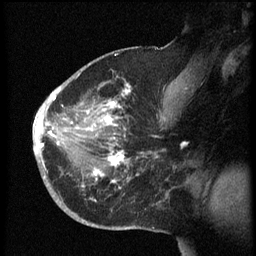
Breast MRI (dynamic contrast-enhanced), one sagittal slice; slice 38 of 60 in the series (ordered by position); dynamic contrast-enhanced series, image 2 of 3 at this slice position (ordered by acquisition); 1.5 T; TE 4.2 ms, TR 8.4 ms; 2.5 mm slice thickness; 256 × 256 image matrix, field of view 200 × 200 mm. Female patient, age 38 years. Case-level facts recorded for this patient, not image findings: setting: breast cancer imaged before/during neoadjuvant chemotherapy; receptor status: HER2-positive.
Structures marked on this image (semi-automatic segmentation, software-assisted and operator-edited):
- analysis volume of interest (the breast-tissue region the enhancement analysis was run in; not a lesion): bounding box [x1, y1, x2, y2] px = [34, 74, 173, 202]
- tumour enhancement mask (voxels above the 70 % enhancement threshold inside the analysis volume of interest): [34, 90, 131, 183]